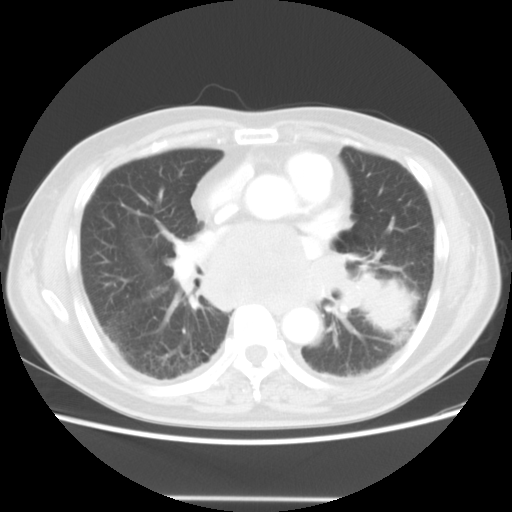
Chest CT, one axial slice. Position 25 of 56 along the scan axis. Reconstruction kernel STANDARD. 140 kVp. Lung window (W 1500 / L -600 HU). 512 × 512 image matrix, field of view 360 × 360 mm. Male patient, age 66 years. From the clinical record (not read from this slice): clinical TNM (as recorded): T4 N3 M0; histopathological grade: G3.
Outlined on this slice (bounding box drawn by a radiologist):
- lung tumour (recorded histology: small cell carcinoma): box from (x=347, y=271) to (x=410, y=337) px